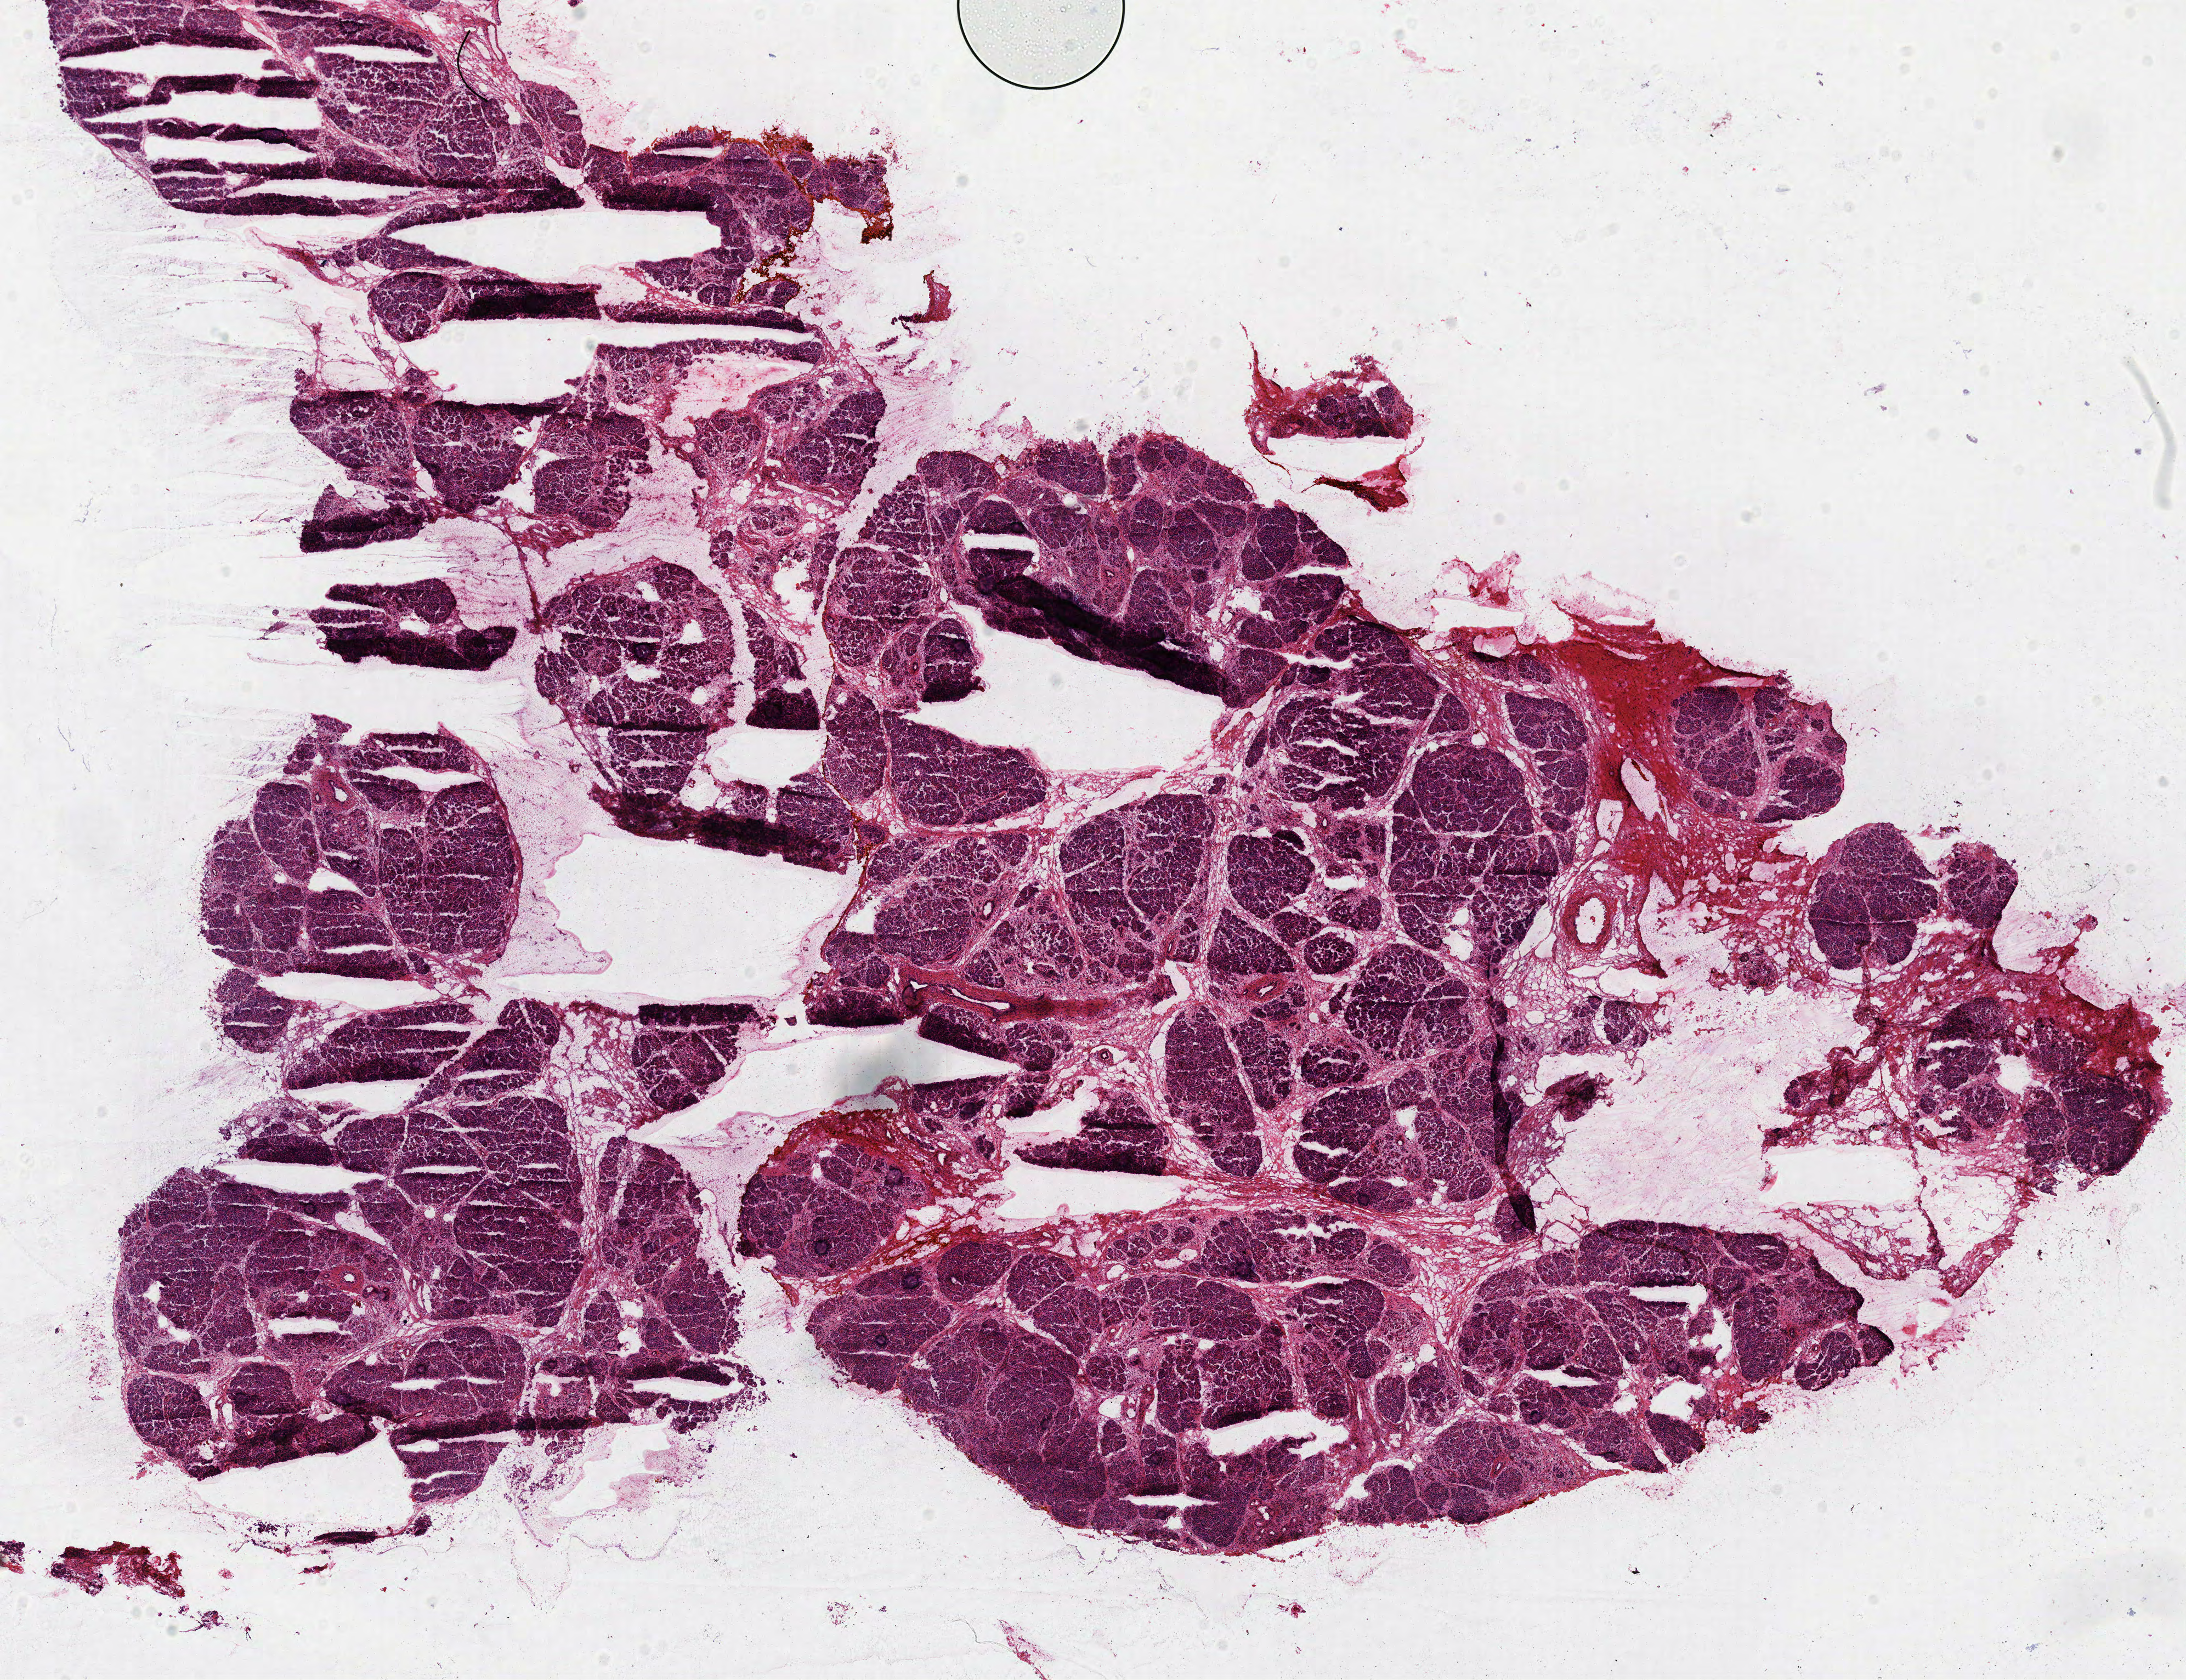
Whole-slide histology image, H&E — low-resolution overview of the scanned area, about 15.7 x 12.1 mm (slide scanned at 40x), frozen section from the top of the tissue portion, solid tissue normal (non-tumour tissue) sample from the pancreas. Patient: female, age at initial diagnosis 59 years.
This section: solid tissue normal sample (biorepository sample class). Patient diagnosis: Infiltrating duct carcinoma, NOS (head of pancreas).